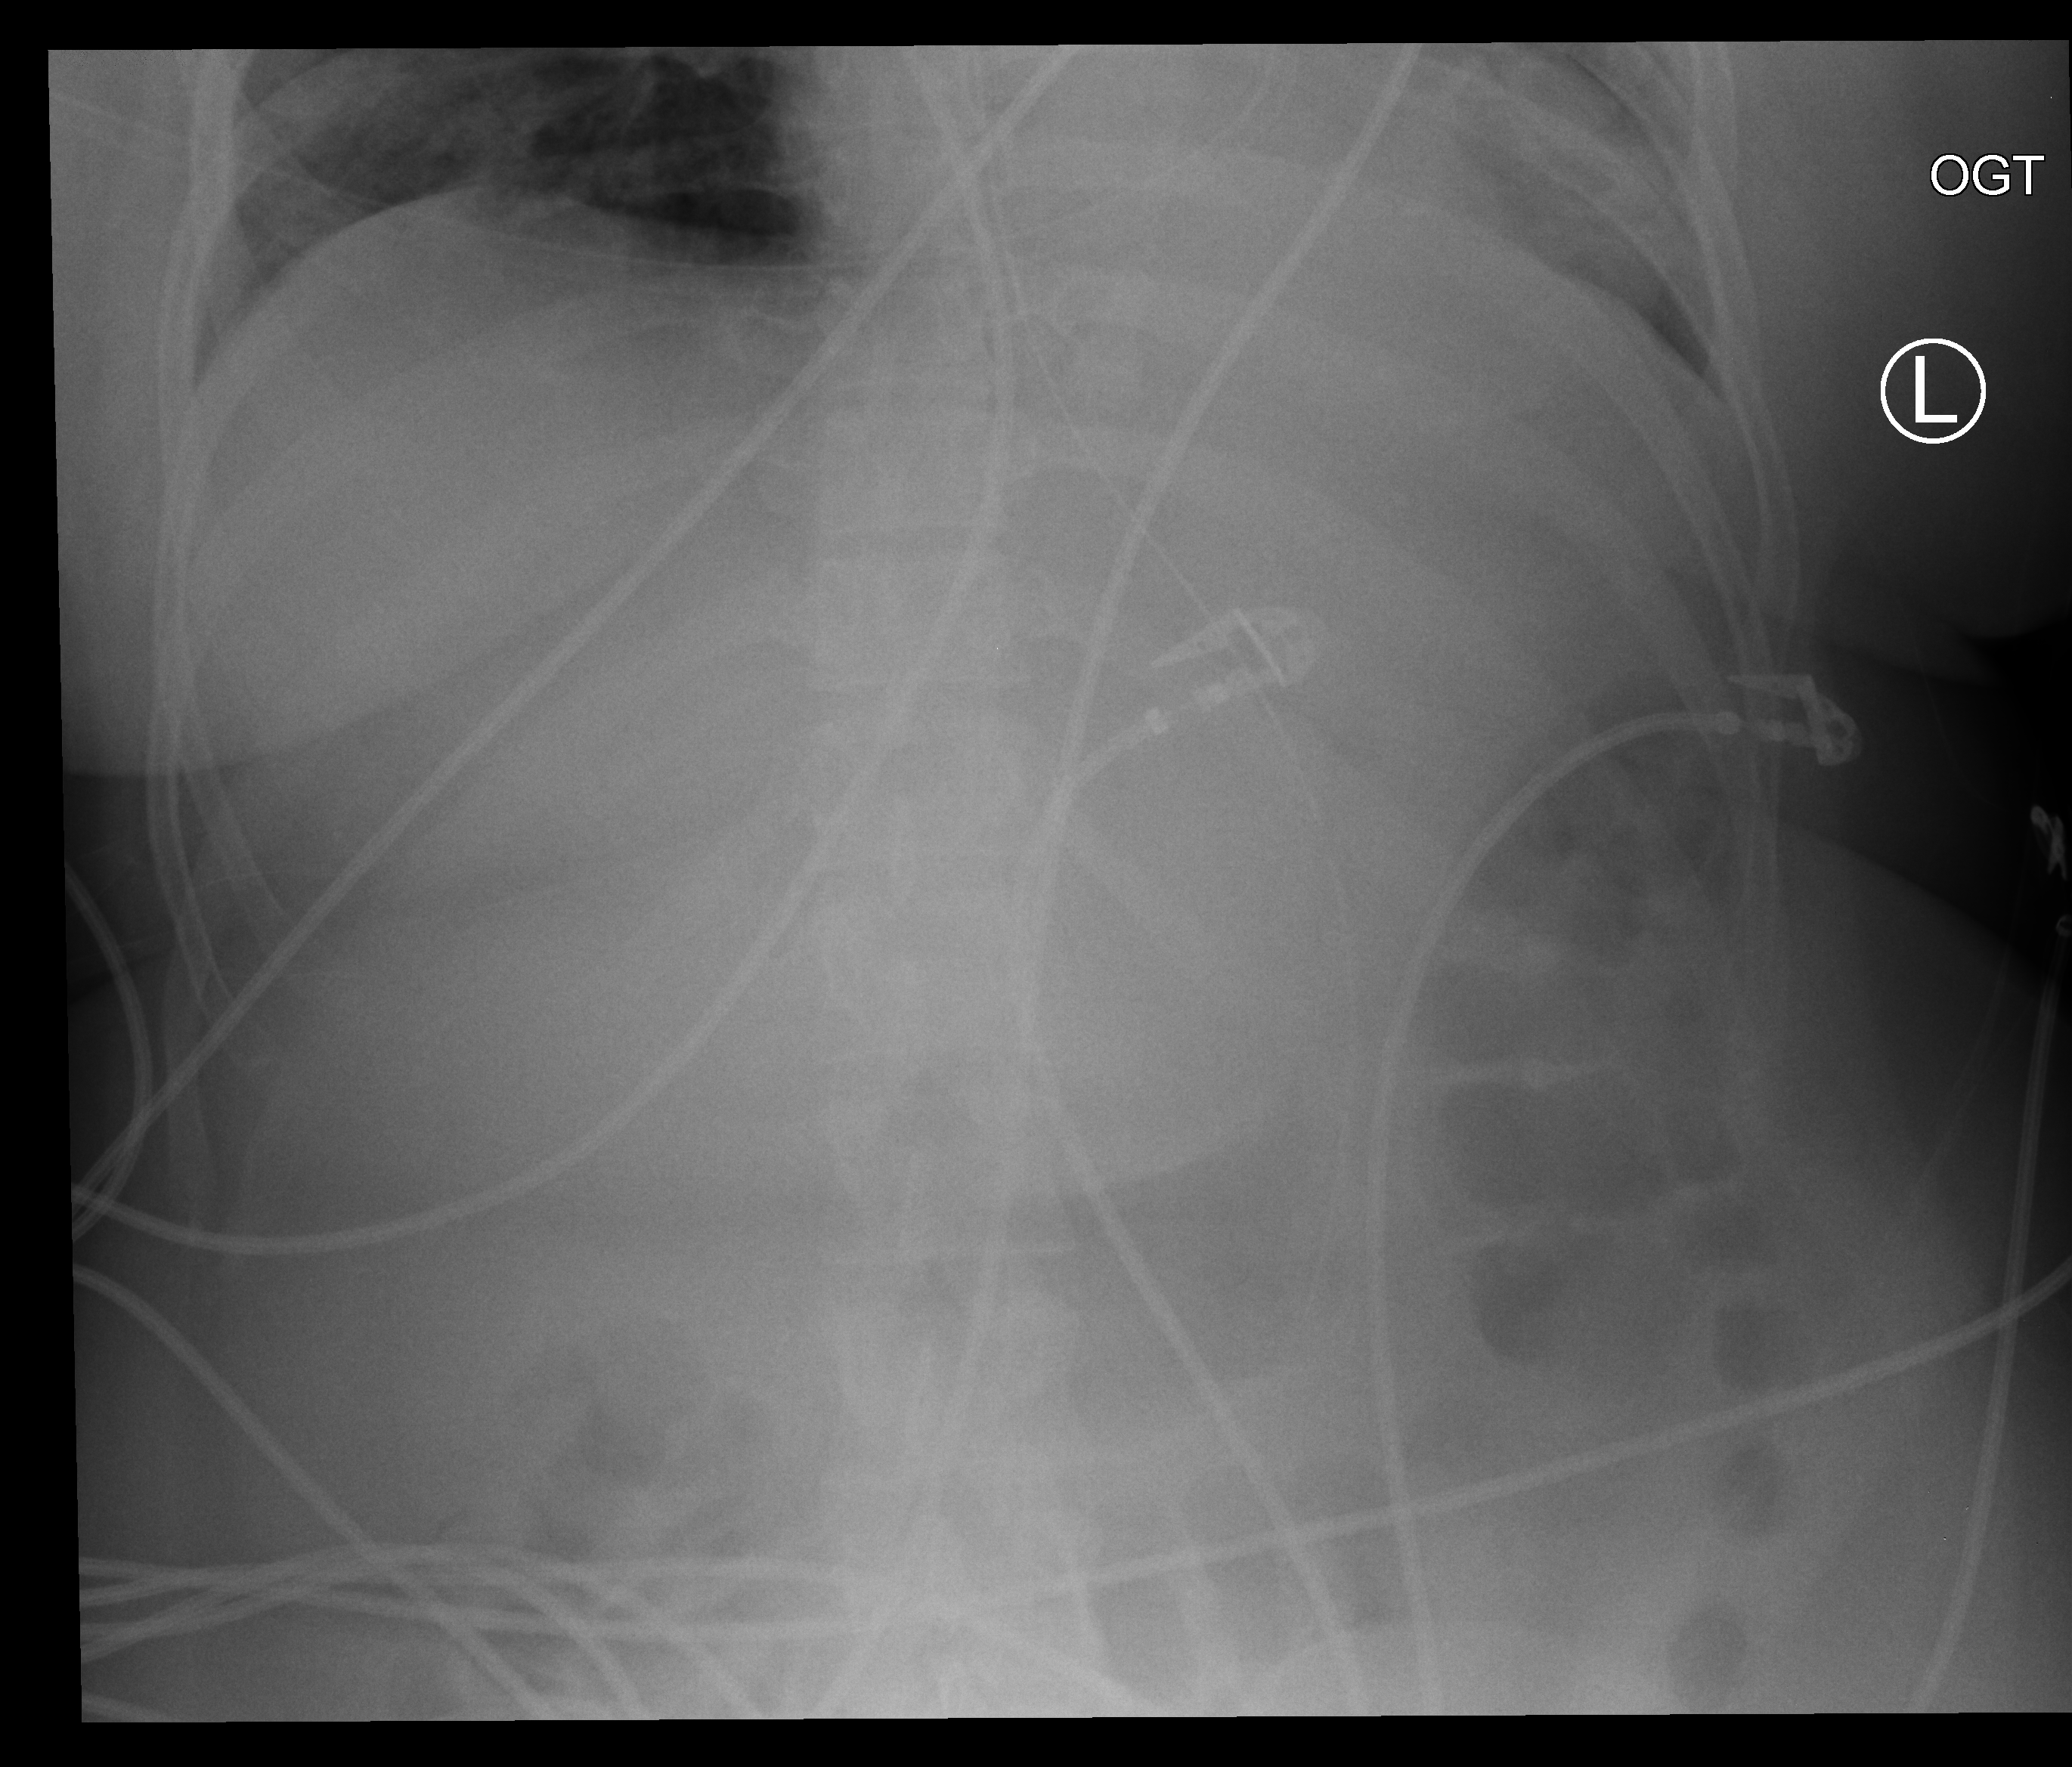
Chest X-ray (portable), anteroposterior (AP) projection. Female patient hospitalised with COVID-19, age 18–59 years.
Hospital-stay facts (about this admission, not read from this image; timing relative to this image not recorded): COPD (admission record): no; admitted to intensive care during this hospital stay: no.